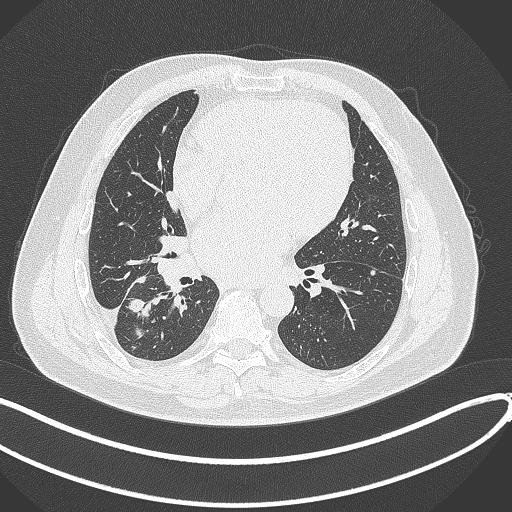
Chest CT, one axial slice. Slice 168 of 360 in the series (ordered by position). Lung window (W 1500 / L -600 HU). 1 mm slice thickness. 512 × 512 image matrix, field of view 400 × 400 mm. Patient: male, 59 years.
Structures marked on this image (bounding box drawn by a radiologist):
- lung tumour (recorded histology: adenocarcinoma): box from (x=128, y=297) to (x=156, y=339) px